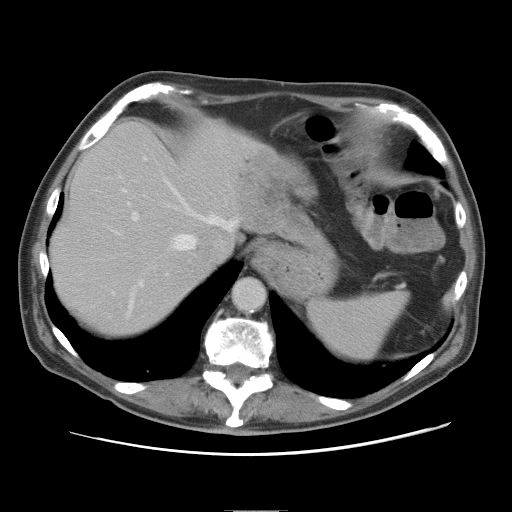
Contrast-enhanced abdominal CT, one axial slice. Position 64 of 89 along the scan axis. 120 kVp. Intravenous contrast given. Soft-tissue window (W 400 / L 40 HU). 5 mm slice thickness. 512 × 512 image matrix. Male patient, age 69 years. Case-level facts recorded for this patient, not image findings: diagnosis: colorectal cancer liver metastases, imaged before liver resection; multiple liver metastases: no; largest metastasis: 8.5 cm.
Outlined on this slice (manually delineated by an expert):
- hepatic veins: box from (x=121, y=178) to (x=238, y=311) px
- liver: (x=53, y=122)–(x=302, y=337)
- planned liver remnant (the part of the liver to remain after resection): (x=52, y=121)–(x=243, y=337)
- portal vein (with intrahepatic branches): (x=132, y=158)–(x=147, y=221)
- liver metastasis: (x=238, y=153)–(x=300, y=224)